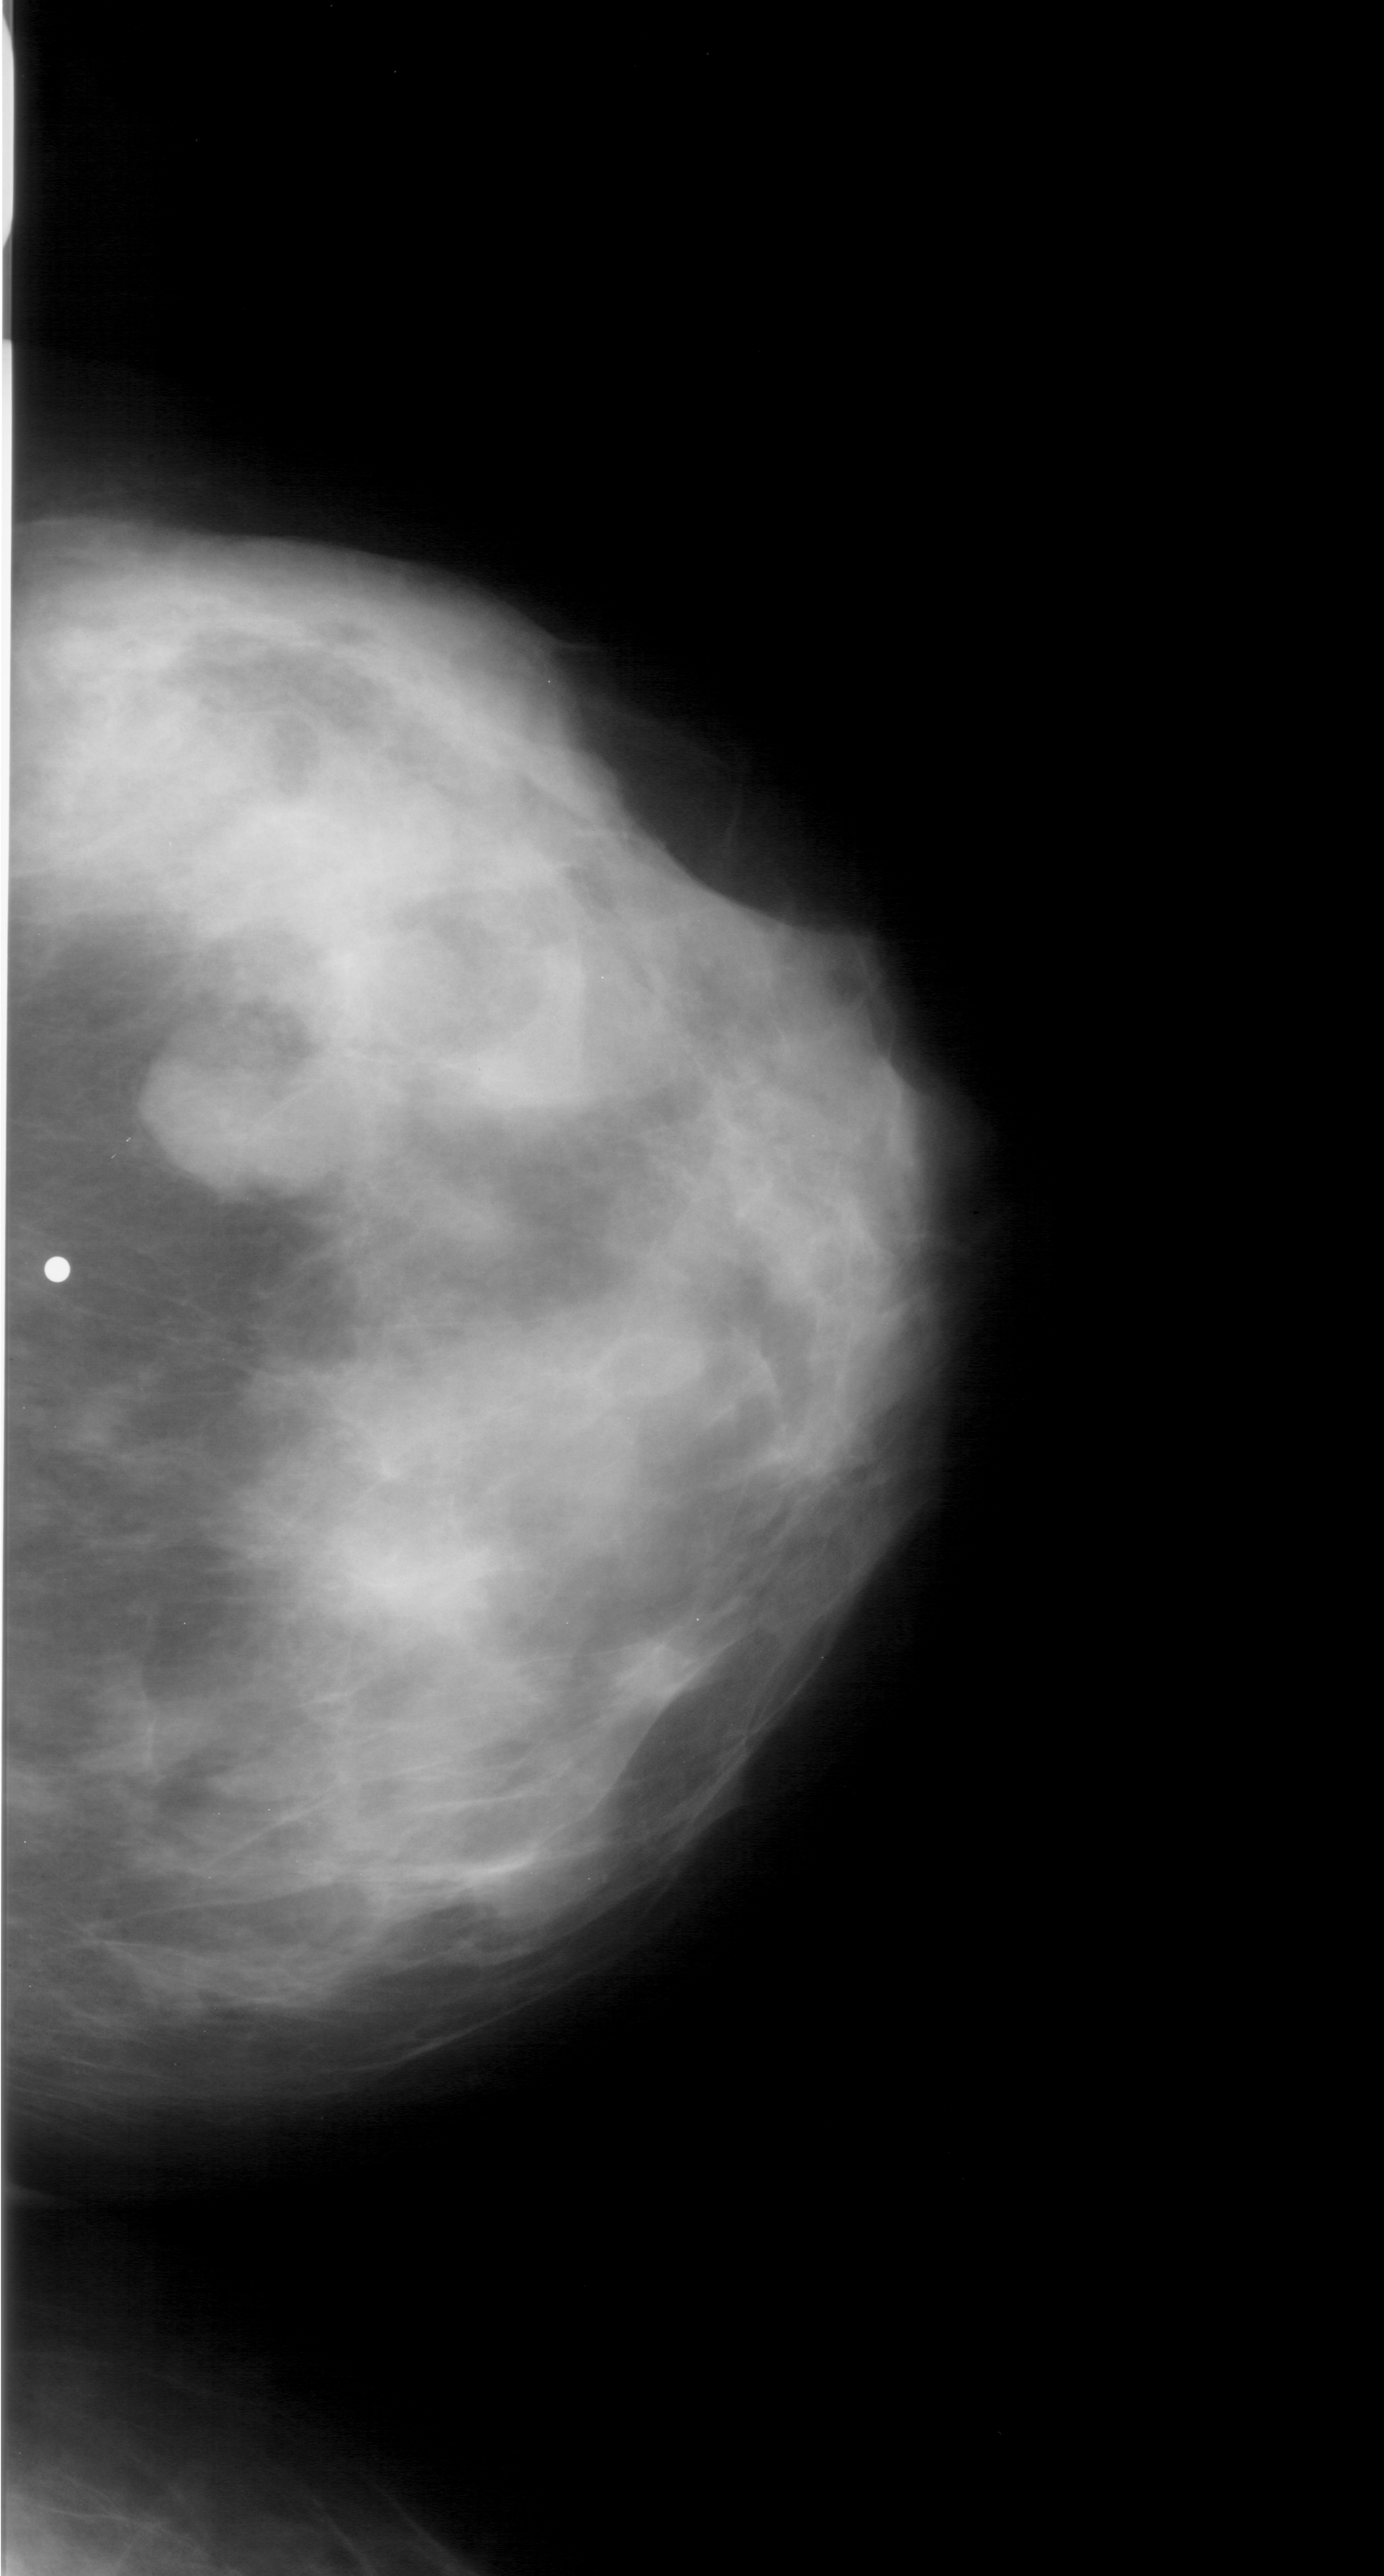
Digitized screen-film mammogram. Right breast. CC view. 1384 × 2576 image matrix.
Marked abnormalities (boxes around the expert regions of interest):
- mass, shape lobulated, margins obscured; BI-RADS assessment category 4; subtlety rating 3 on a 1 (subtle) to 5 (obvious) scale; pathology (as recorded): benign: bounding box <141,993,341,1217> (left, top, right, bottom; pixels)